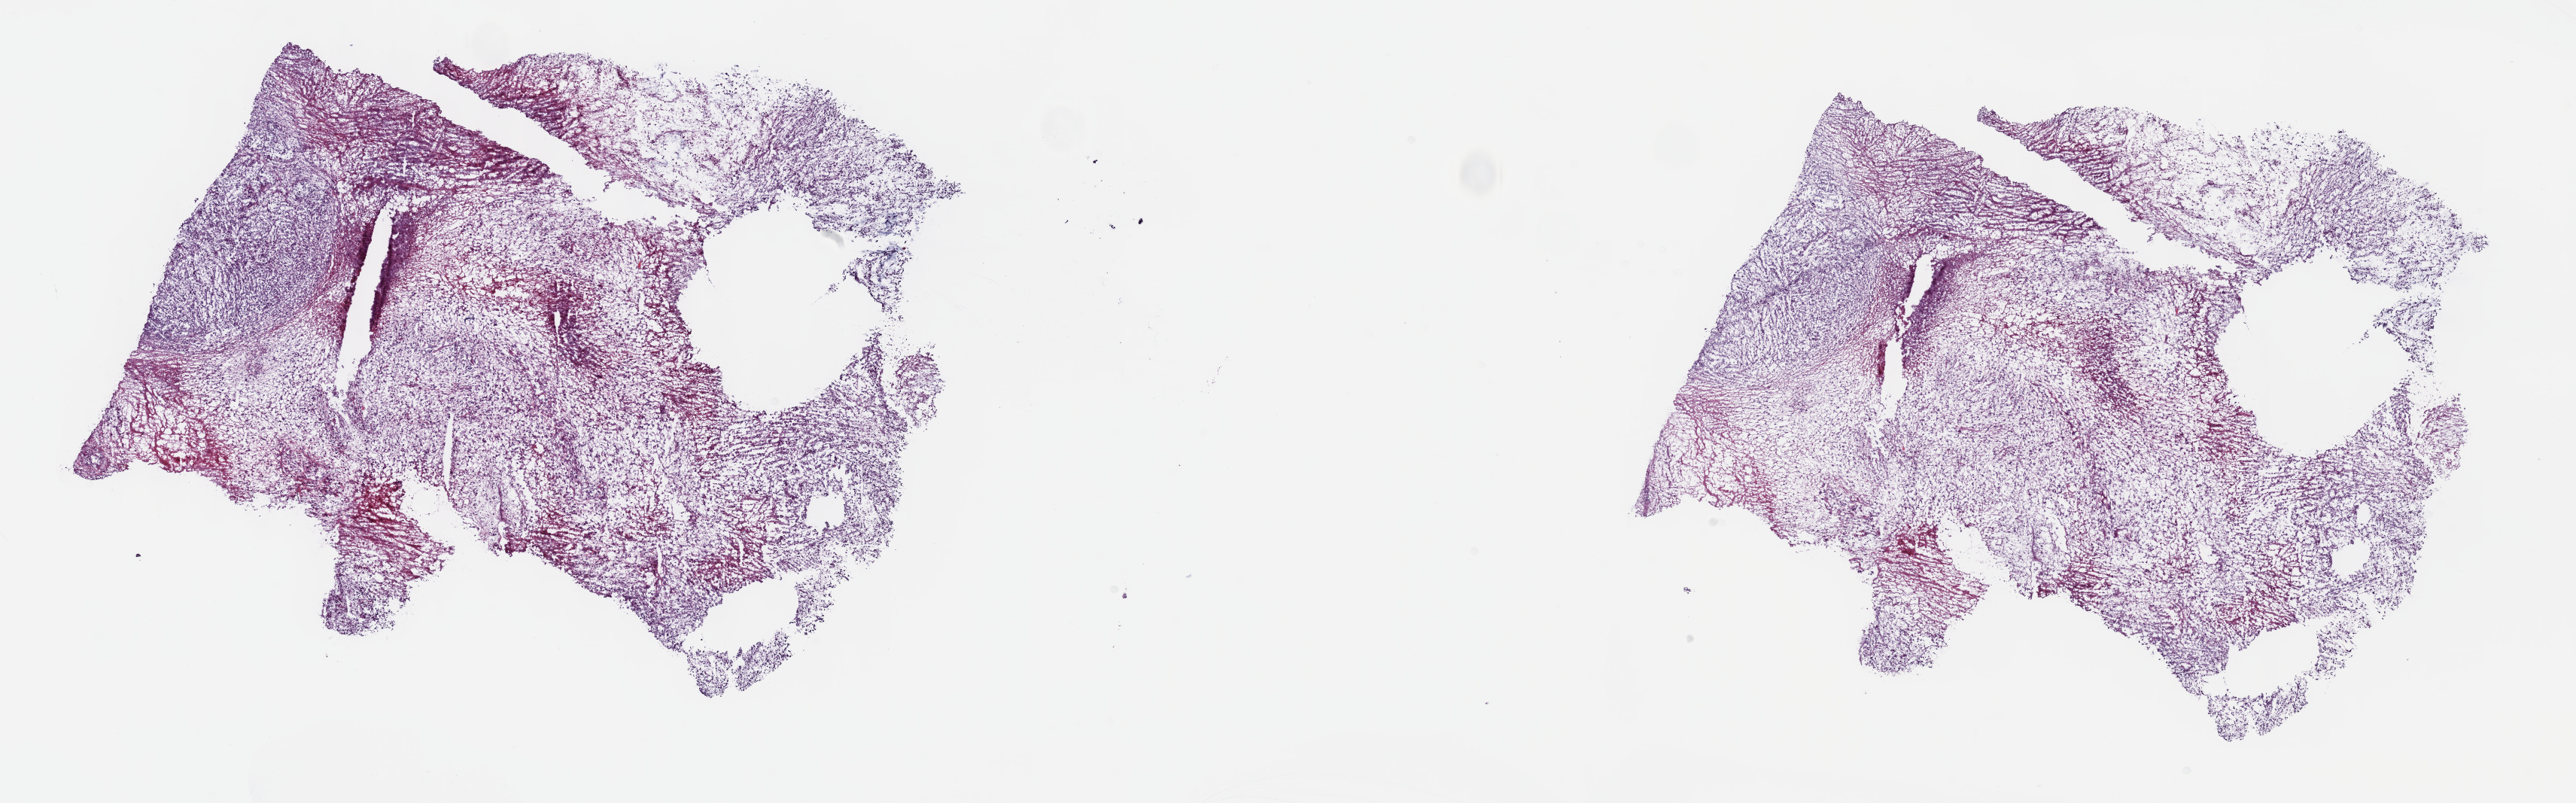
Digitized H&E tissue section (whole slide) — low-resolution overview of the scanned area, about 27.7 x 8.6 mm, frozen section from the top of the tissue portion, connective, subcutaneous and other soft tissues, primary tumour sample. Male, age 60 years at initial diagnosis. Composition of this section per pathologist review: tumour cells 65%, tumour nuclei 65%, normal cells 0%, stromal cells 20%, necrosis 15%. Inflammatory infiltration, as recorded: lymphocyte infiltration 3%, monocyte infiltration 2%, neutrophil infiltration 3%.
Diagnosis: Fibromyxosarcoma.